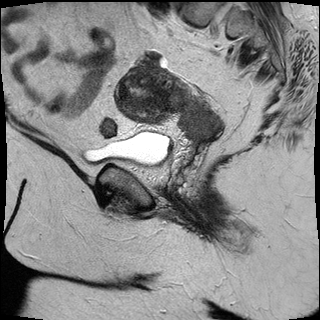
Pelvic MRI for cervical cancer, one sagittal slice; slice 11 of 30 in the series (ordered by position); T2-weighted; 1.5 T; TE 89 ms, TR 2930 ms; 4 mm slice thickness; 320 × 320 image matrix, field of view 260 × 260 mm. Female patient, age 53 years.
Outlined on this slice (expert manual segmentation):
- uterus and cervix: box from (x=114, y=65) to (x=222, y=144) px